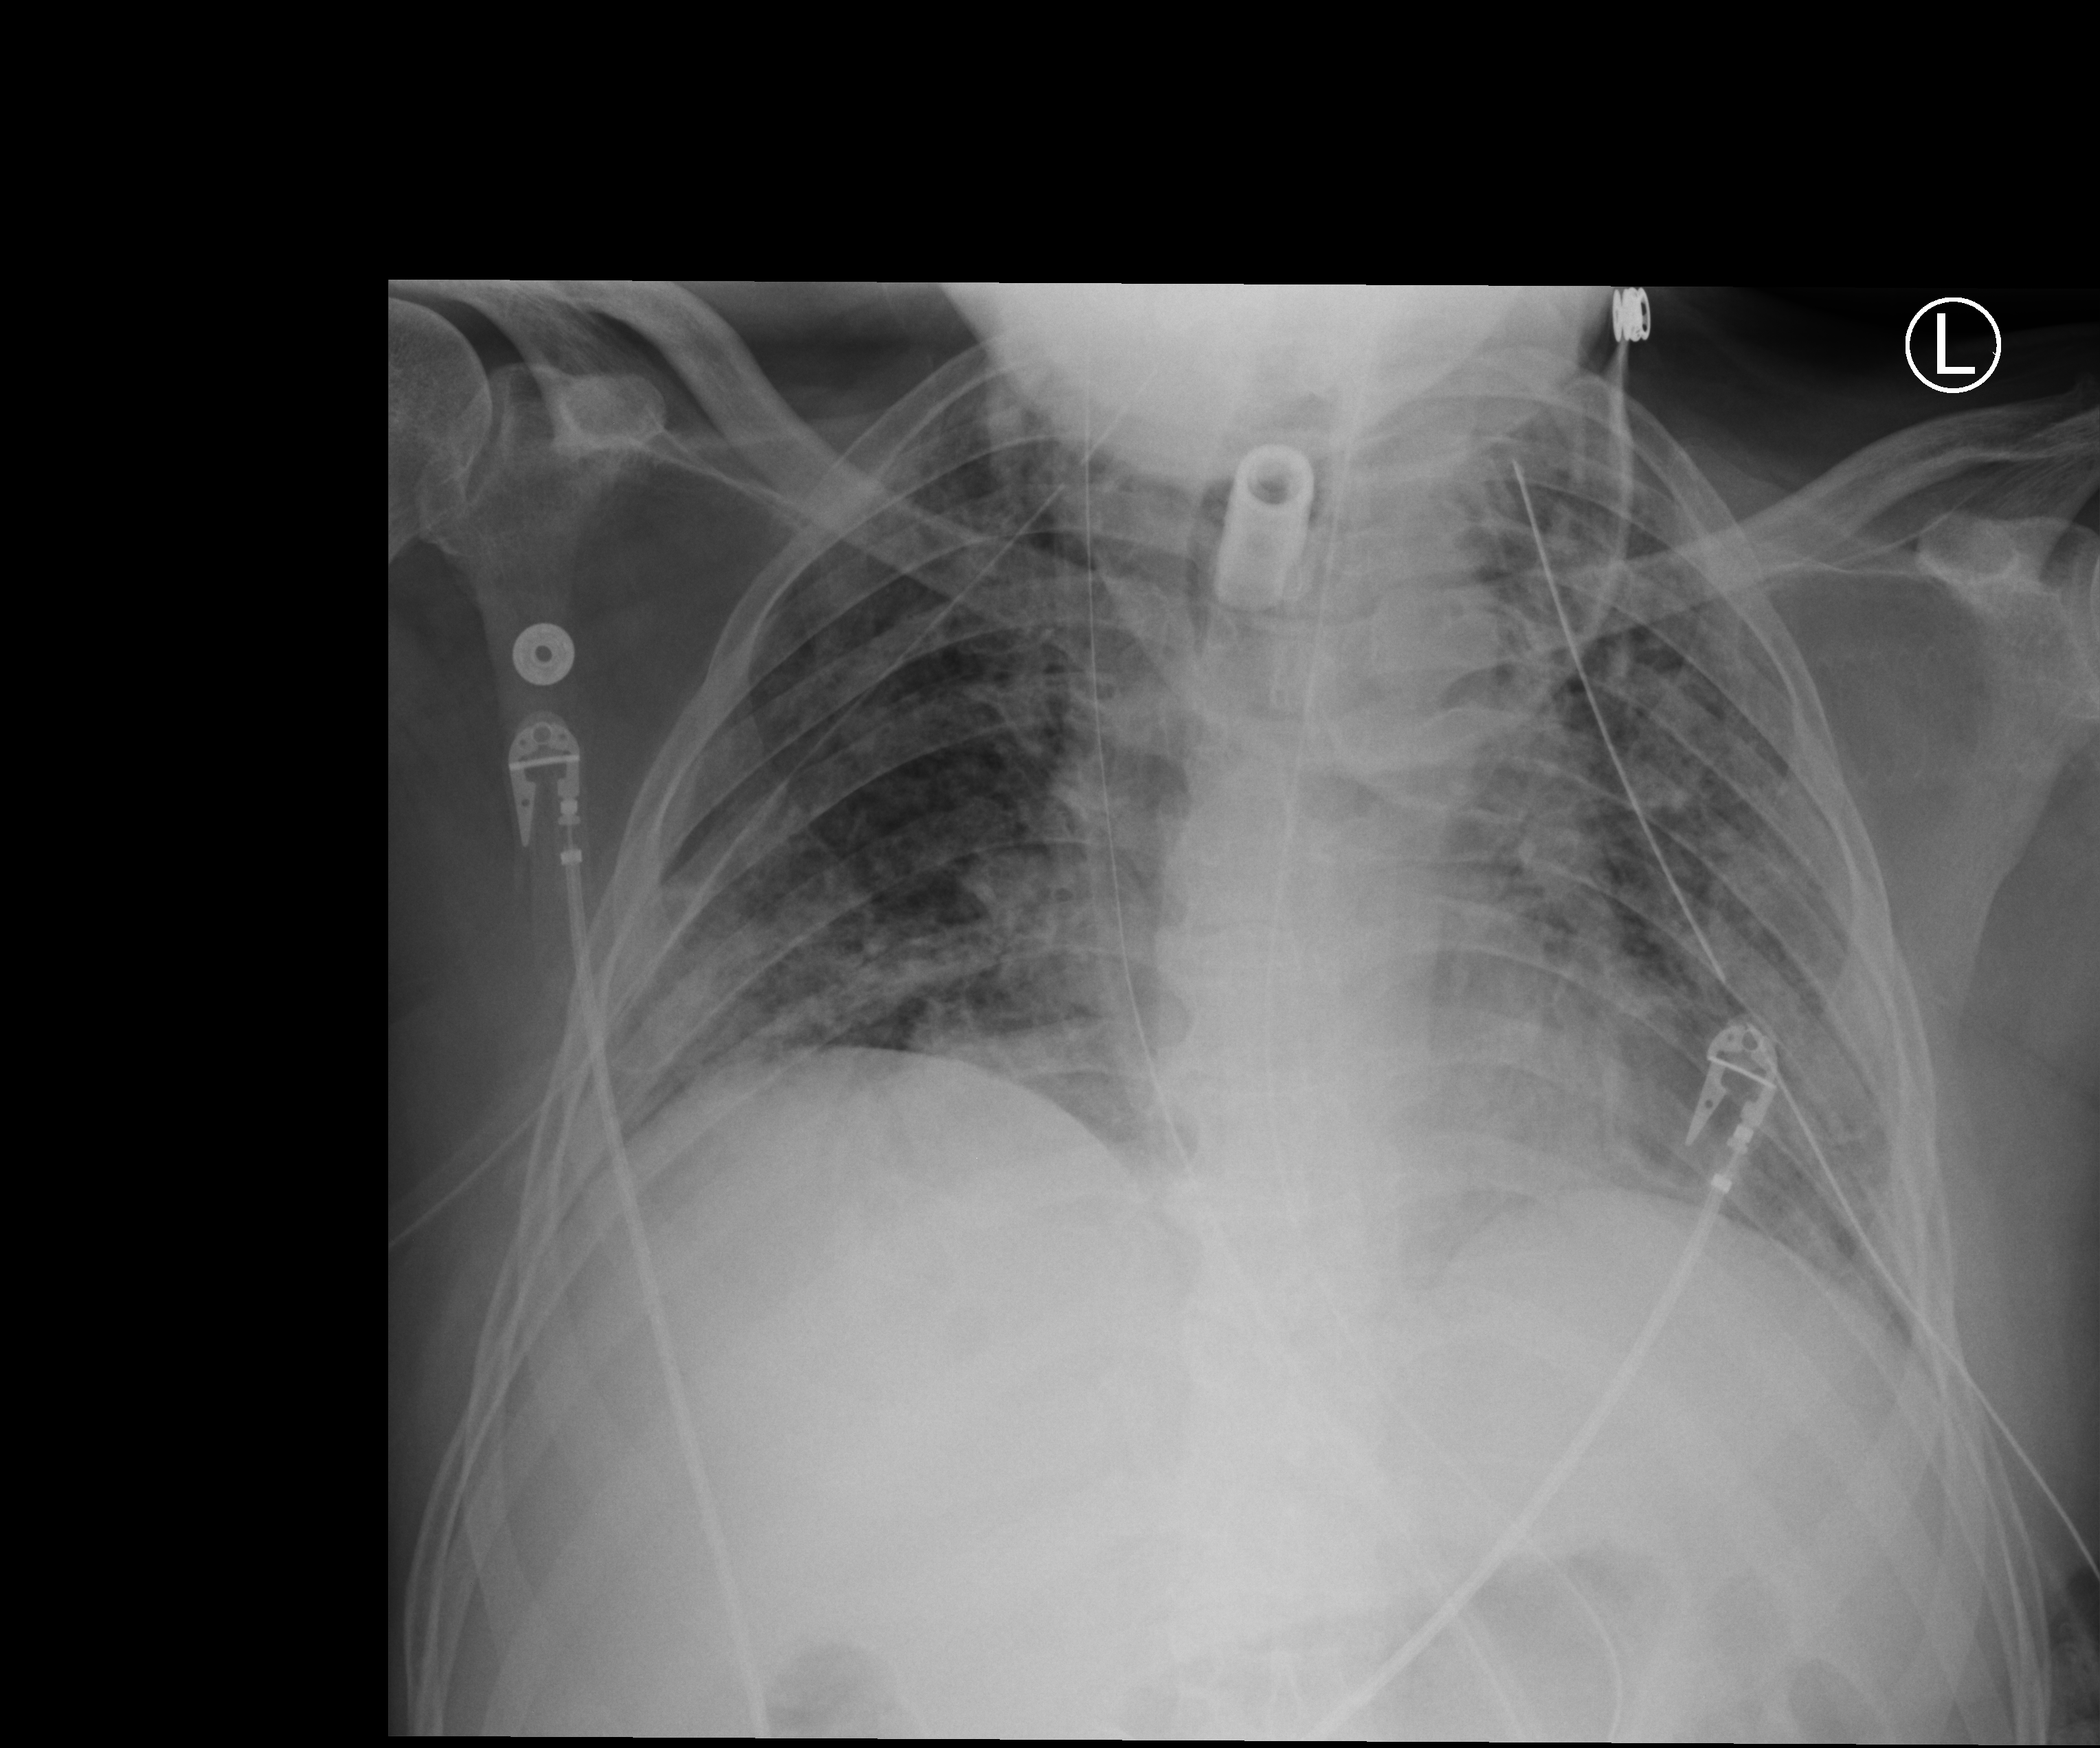
Bedside chest radiograph (computed radiography), anteroposterior (AP) projection. Male patient hospitalised with COVID-19, age 18–59 years.
Hospital-stay facts (about this admission, not read from this image; timing relative to this image not recorded): mechanically ventilated during this hospital stay: yes.